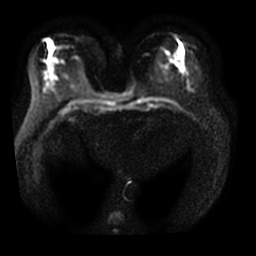
Breast MRI, one axial slice. Slice 14 of 34 in the series (ordered by position). Diffusion-weighted series; image 2 of 4 stored at this slice position (different b-values; order by instance number). 3 T. 5 mm slice thickness. 256 × 256 image matrix. Female patient.
Annotated regions visible in this slice (manually delineated by an expert):
- tumour on diffusion-weighted imaging: bounding box (x1, y1, x2, y2) in pixels: (179, 46, 182, 55)